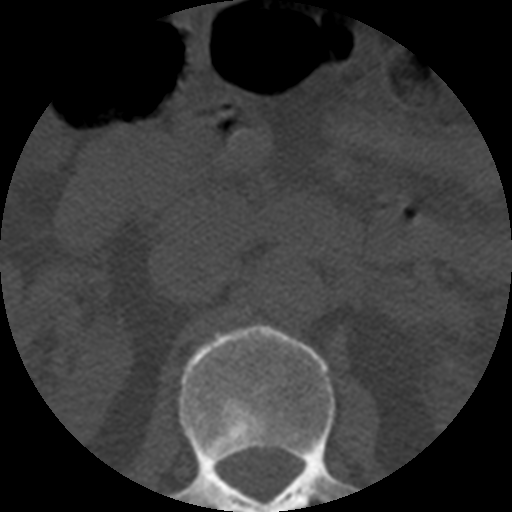
CT including the spine, one axial slice. Position 179 of 508 along the scan axis. Reconstruction kernel STANDARD. 120 kVp. Bone window (W 1800 / L 400 HU). 1.25 mm slice thickness. 512 × 512 image matrix, field of view 160 × 160 mm. Patient age 57 years. Case-level facts recorded for this patient, not image findings: primary cancer: prostate.
Outlined on this slice (semi-automatically segmented with operator editing):
- L1 vertebra: bounding box <171,325,356,512> (left, top, right, bottom; pixels)